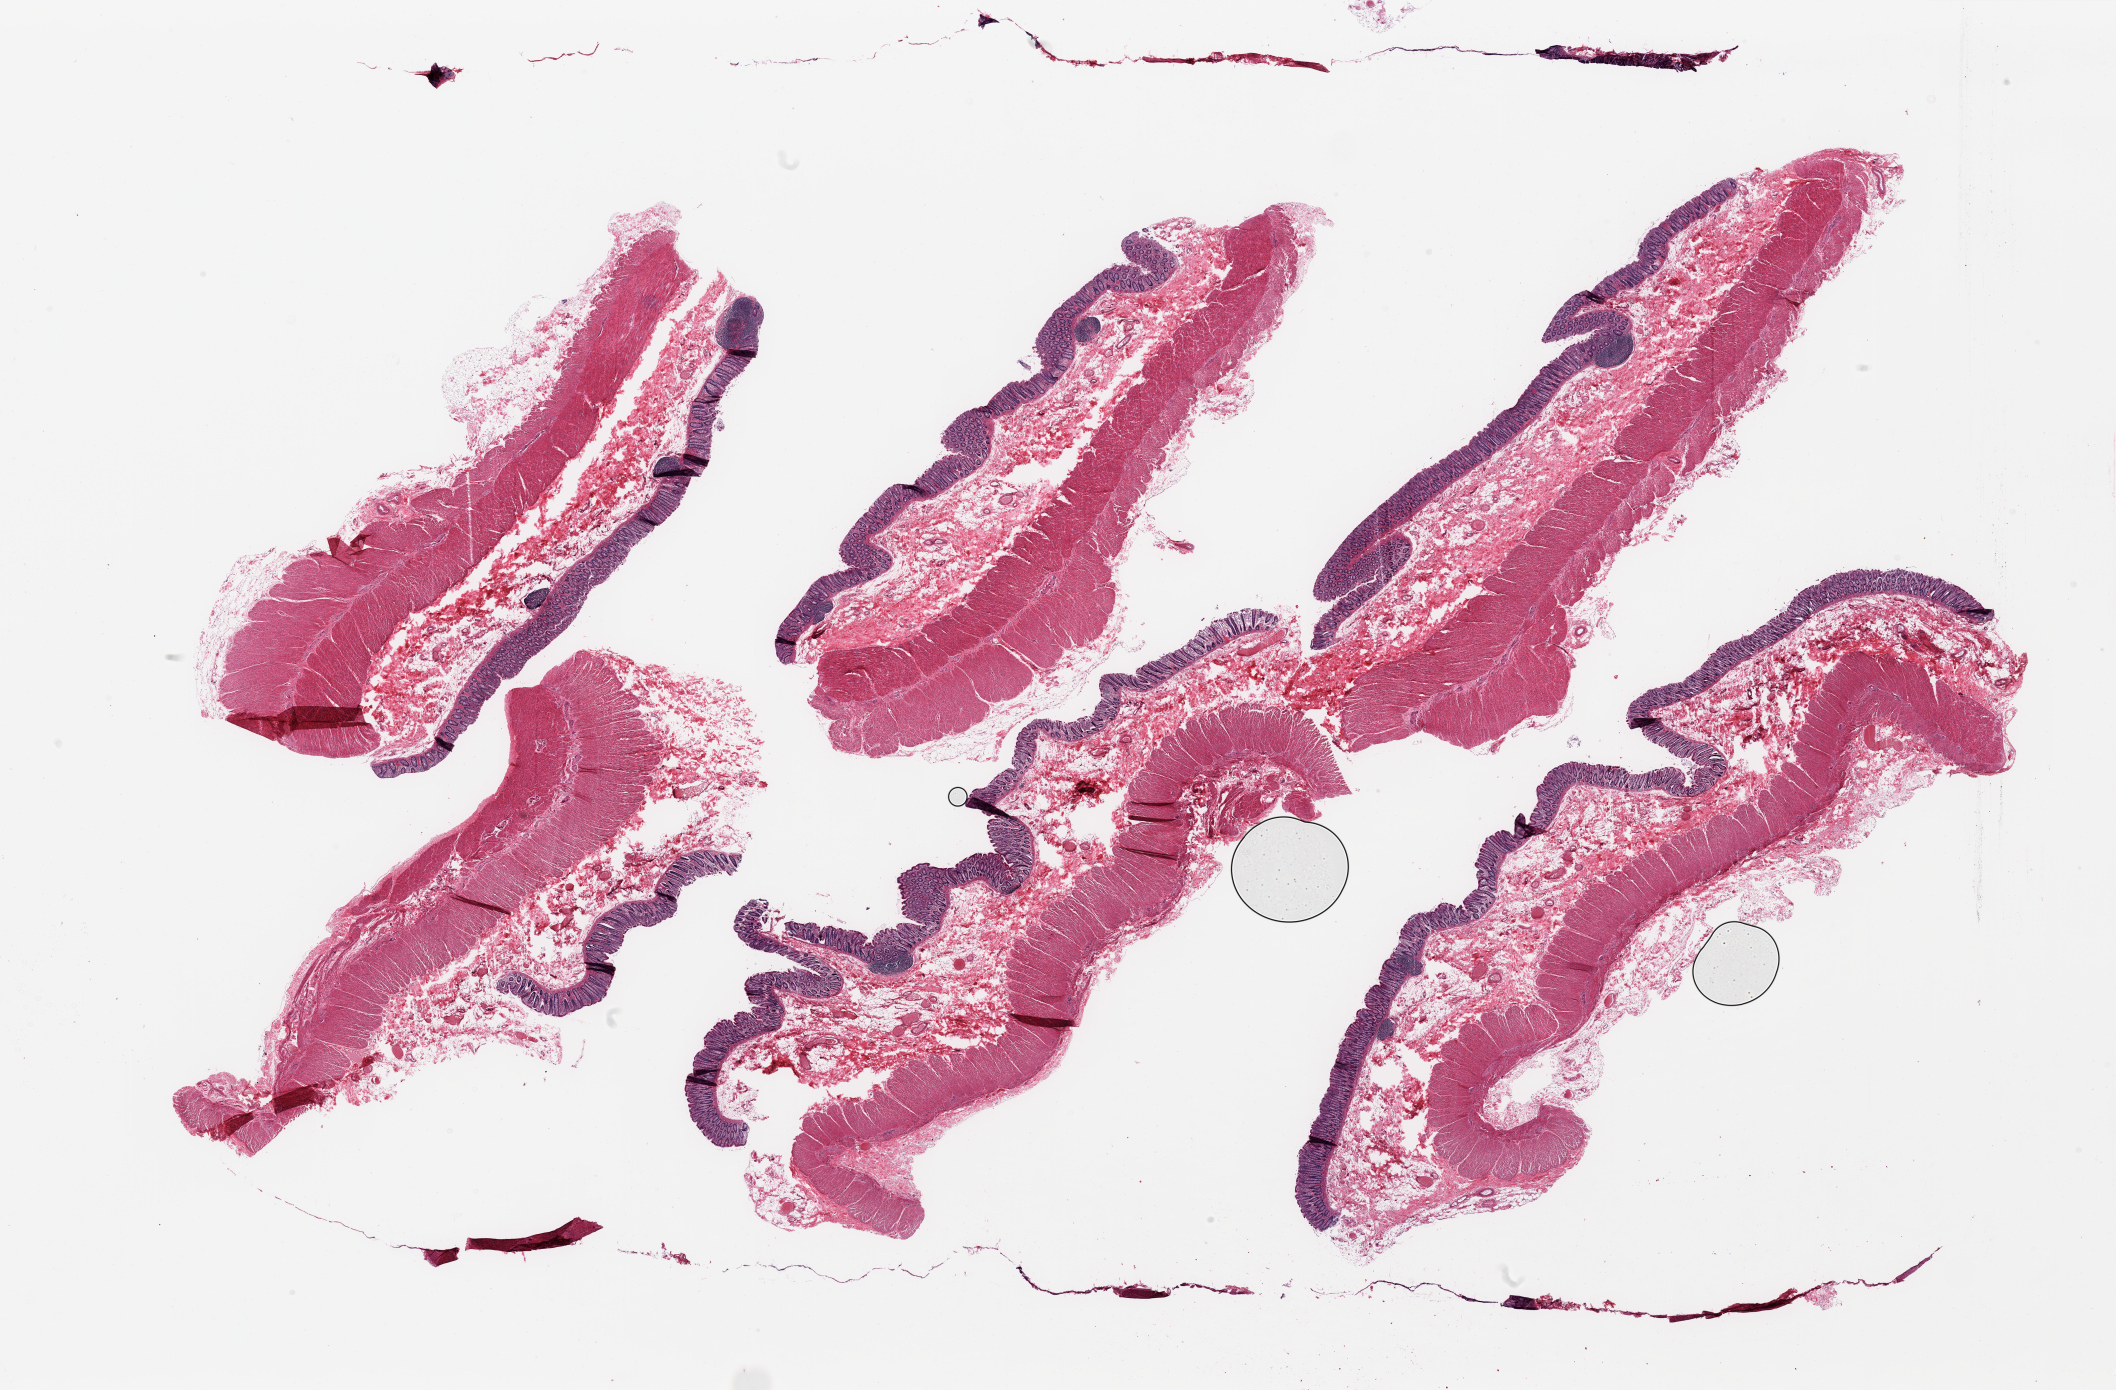
H&E whole-slide image, low-resolution overview of the scanned area, about 33.5 x 22.0 mm, PAXgene-fixed, paraffin-embedded tissue, section of transverse colon (target tissue), tissue donor sample. Male donor.
* reviewer comment on this tissue sample: 6 pieces; full thickness sections